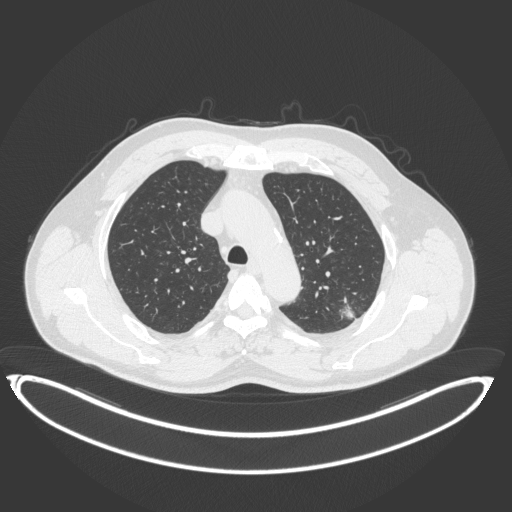
Chest CT, one axial slice; slice 270 of 399 in the series (ordered by position); reconstruction kernel B31f; lung window (W 1500 / L -600 HU); 1 mm slice thickness; 512 × 512 image matrix. Patient: male, 58 years. From the clinical record (not read from this slice): clinical TNM (as recorded): T1c N0 M0; histopathological grade: G1-2.
Annotated regions visible in this slice (bounding box drawn by a radiologist):
- lung tumour (recorded histology: adenocarcinoma): bounding box [x1, y1, x2, y2] px = [338, 301, 362, 328]